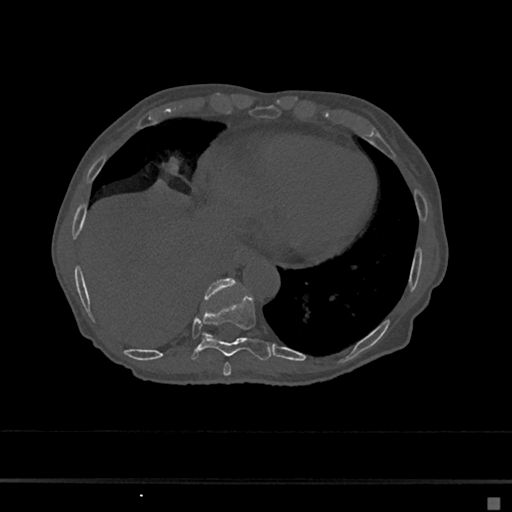
CT including the spine, one axial slice. Reconstruction kernel Br40s/3. Bone window (W 1800 / L 400 HU). 0.5 mm slice thickness. 512 × 512 image matrix, field of view 360 × 360 mm. Female patient, age 68 years. From the clinical record (not read from this slice): primary cancer: renal.
Annotated regions visible in this slice (semi-automatic segmentation, software-assisted and operator-edited):
- T10 vertebra: bounding box <204,279,235,336> (left, top, right, bottom; pixels)
- T8 vertebra: <223,363,231,377>
- T9 vertebra: <190,294,273,360>